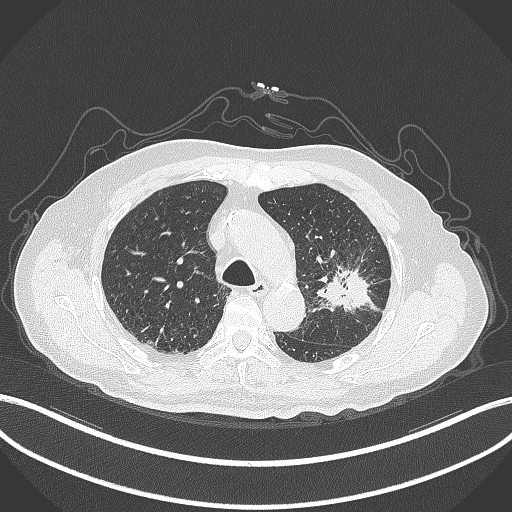
Chest CT, one axial slice. Position 210 of 331 along the scan axis. Reconstruction kernel B70f. 120 kVp. Lung window (W 1500 / L -600 HU). 1 mm slice thickness. 512 × 512 image matrix, field of view 400 × 400 mm. Patient: male, 79 years. Case-level facts recorded for this patient, not image findings: clinical TNM (as recorded): T2a N1 M1; histopathological grade: G3.
Outlined on this slice (bounding box drawn by a radiologist):
- lung tumour (recorded histology: adenocarcinoma): bounding box [x1, y1, x2, y2] px = [310, 261, 380, 318]